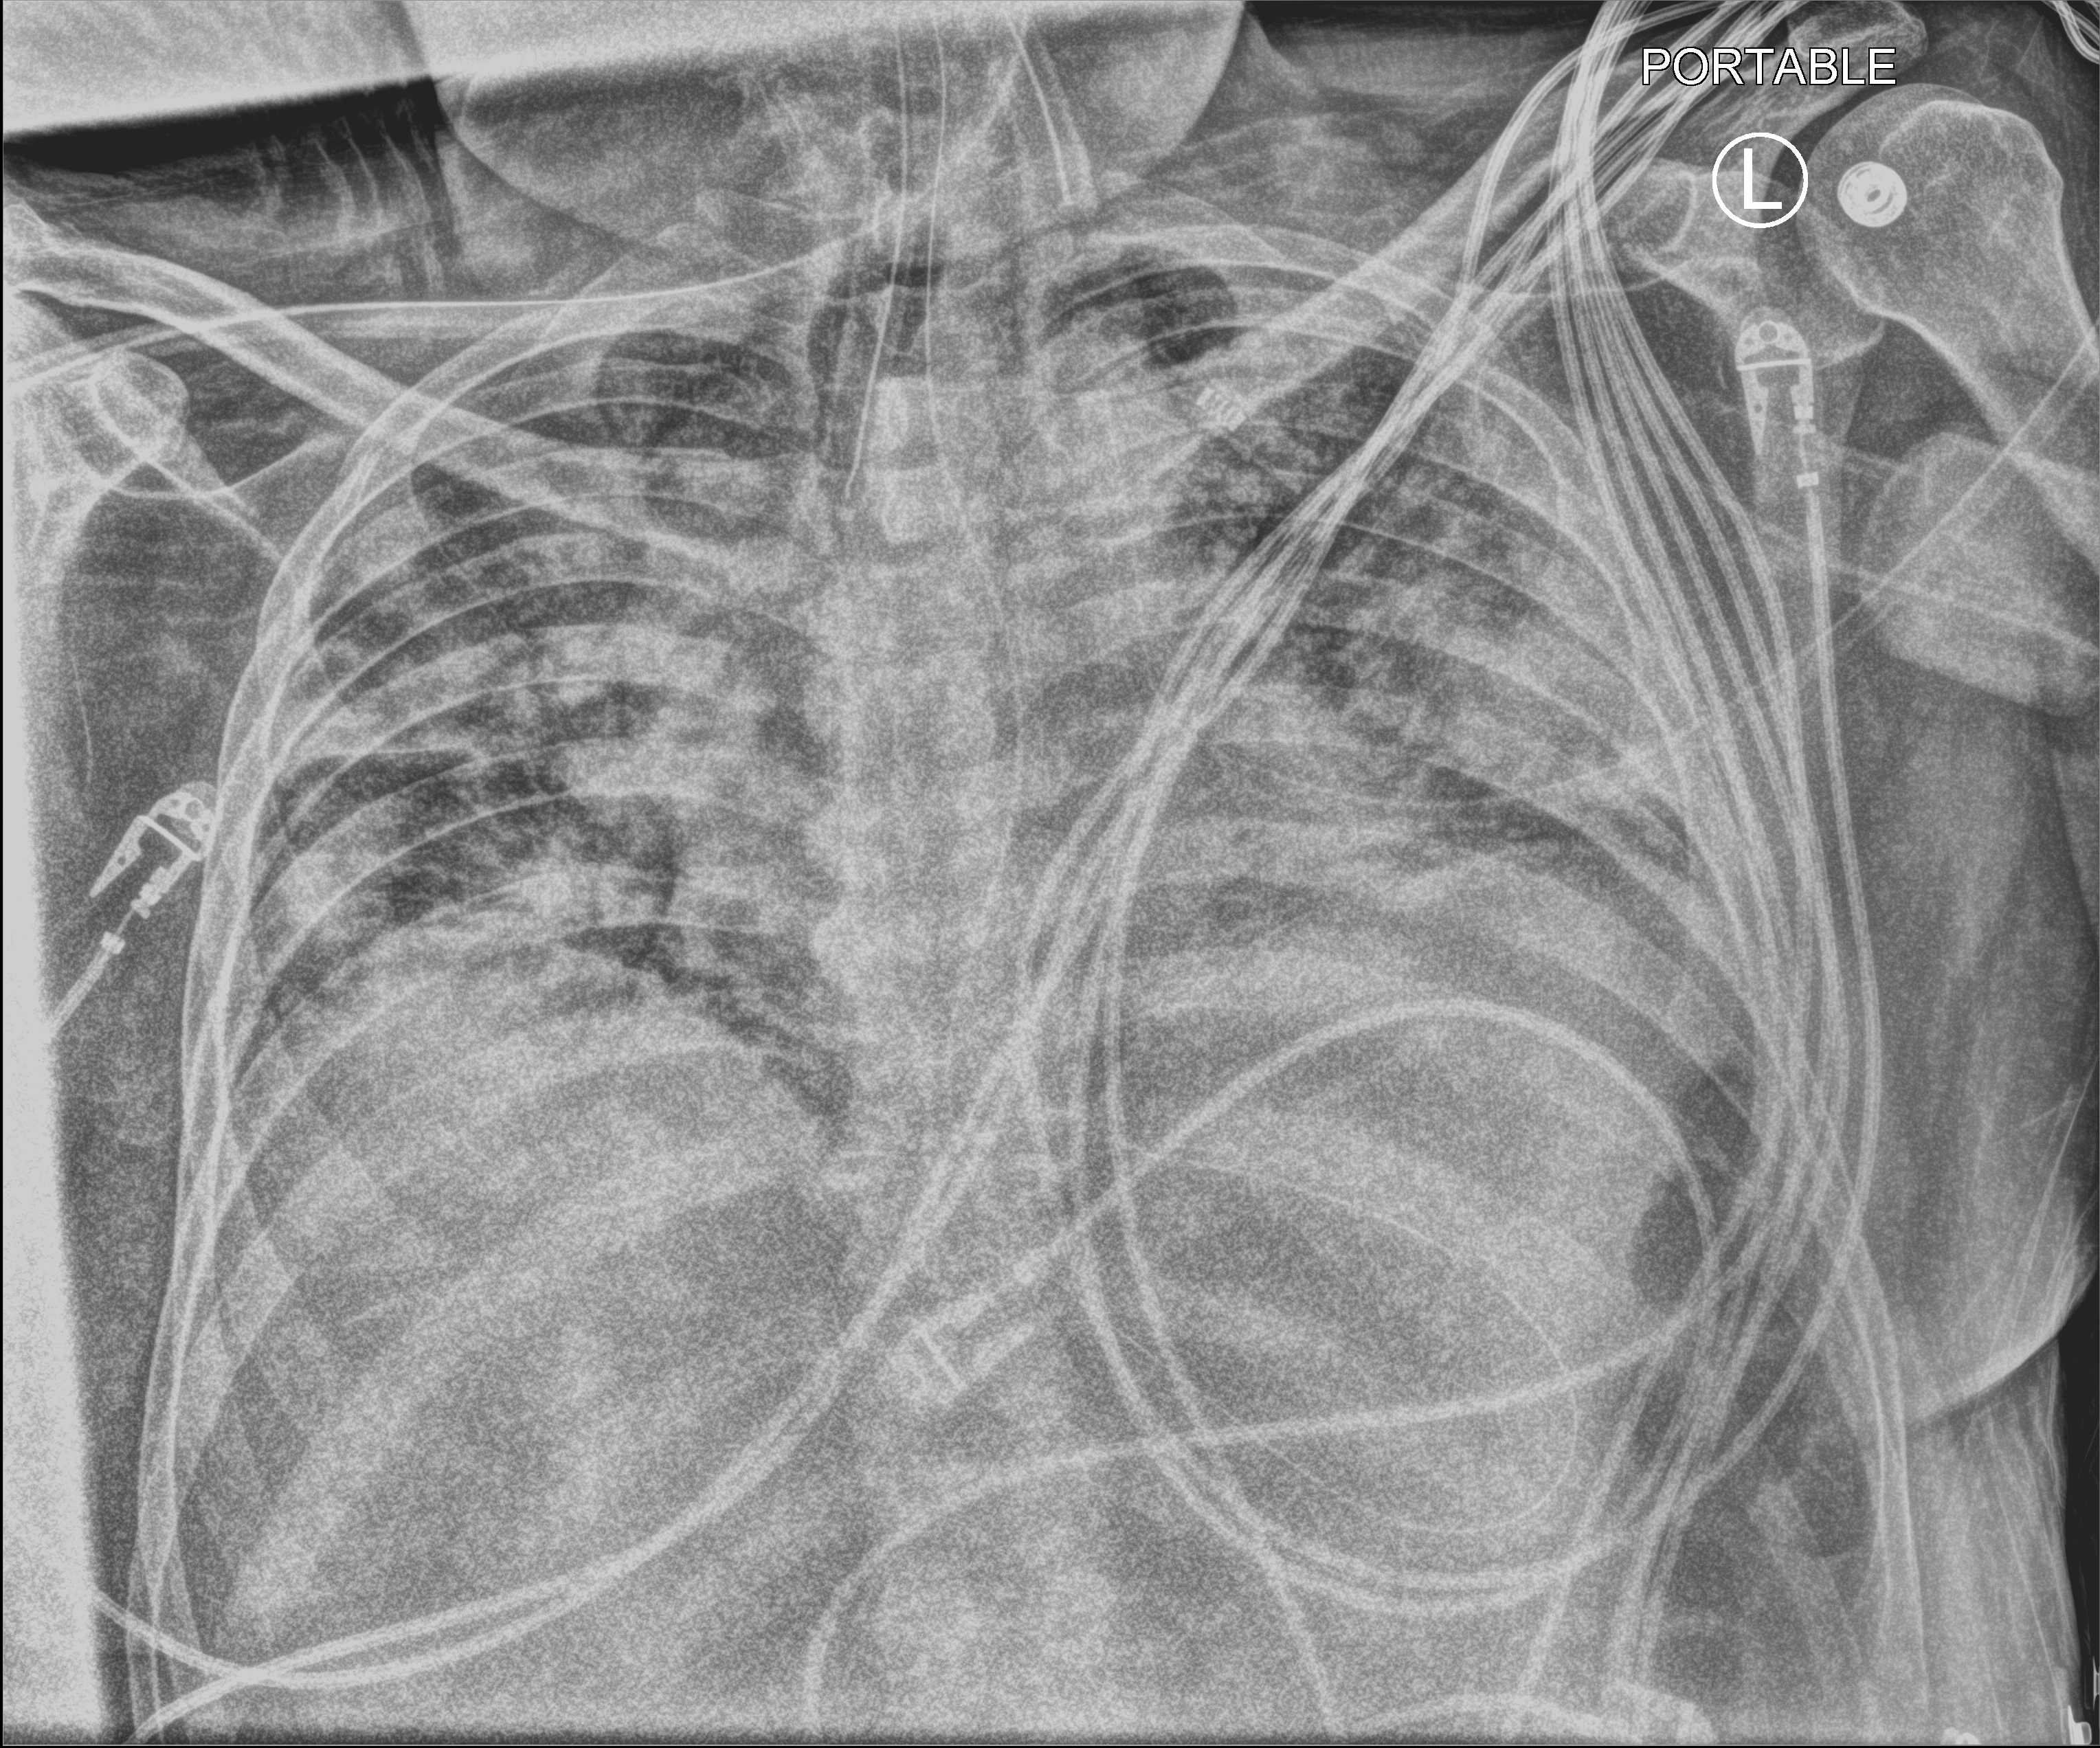
Chest X-ray (portable). Patient hospitalised with COVID-19; male, aged 60–74 years.
From the hospital-stay record, not from the radiograph (when in the stay this image was taken is not recorded): mechanically ventilated during this hospital stay: yes; chronic kidney disease (admission record): no.